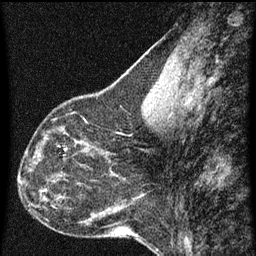
Breast MRI (dynamic contrast-enhanced), one sagittal slice; position 27 of 60 along the scan axis; dynamic contrast-enhanced series, image 2 of 3 at this slice position (ordered by acquisition); 1.5 T; TE 4.2 ms, TR 8 ms; 256 × 256 image matrix. Female patient, age 44 years.
Outlined on this slice (semi-automatically segmented with operator editing):
- analysis volume of interest (the breast-tissue region the enhancement analysis was run in; not a lesion): bounding box (x1, y1, x2, y2) in pixels: (49, 128, 95, 169)
- tumour enhancement mask (voxels above the 70 % enhancement threshold inside the analysis volume of interest): (73, 140, 86, 157)